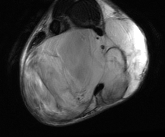
MRI of an extremity soft-tissue mass, one axial slice. Position 26 of 81 along the scan axis. T2-weighted fat-saturated. MR volume resampled by the dataset authors to the PET/CT grid (not the native acquisition matrix). 3.27 mm slice thickness. 165 × 137 image matrix, field of view 161 × 134 mm. Male patient. Case-level facts recorded for this patient, not image findings: histological type: liposarcoma - round cell; grade: high; site of the primary tumour: right calf.
Structures marked on this image (expert contour drawn on MRI and transferred to this co-registered scan by the dataset authors):
- gross tumour volume (mass): bounding box <21,18,147,119> (left, top, right, bottom; pixels)